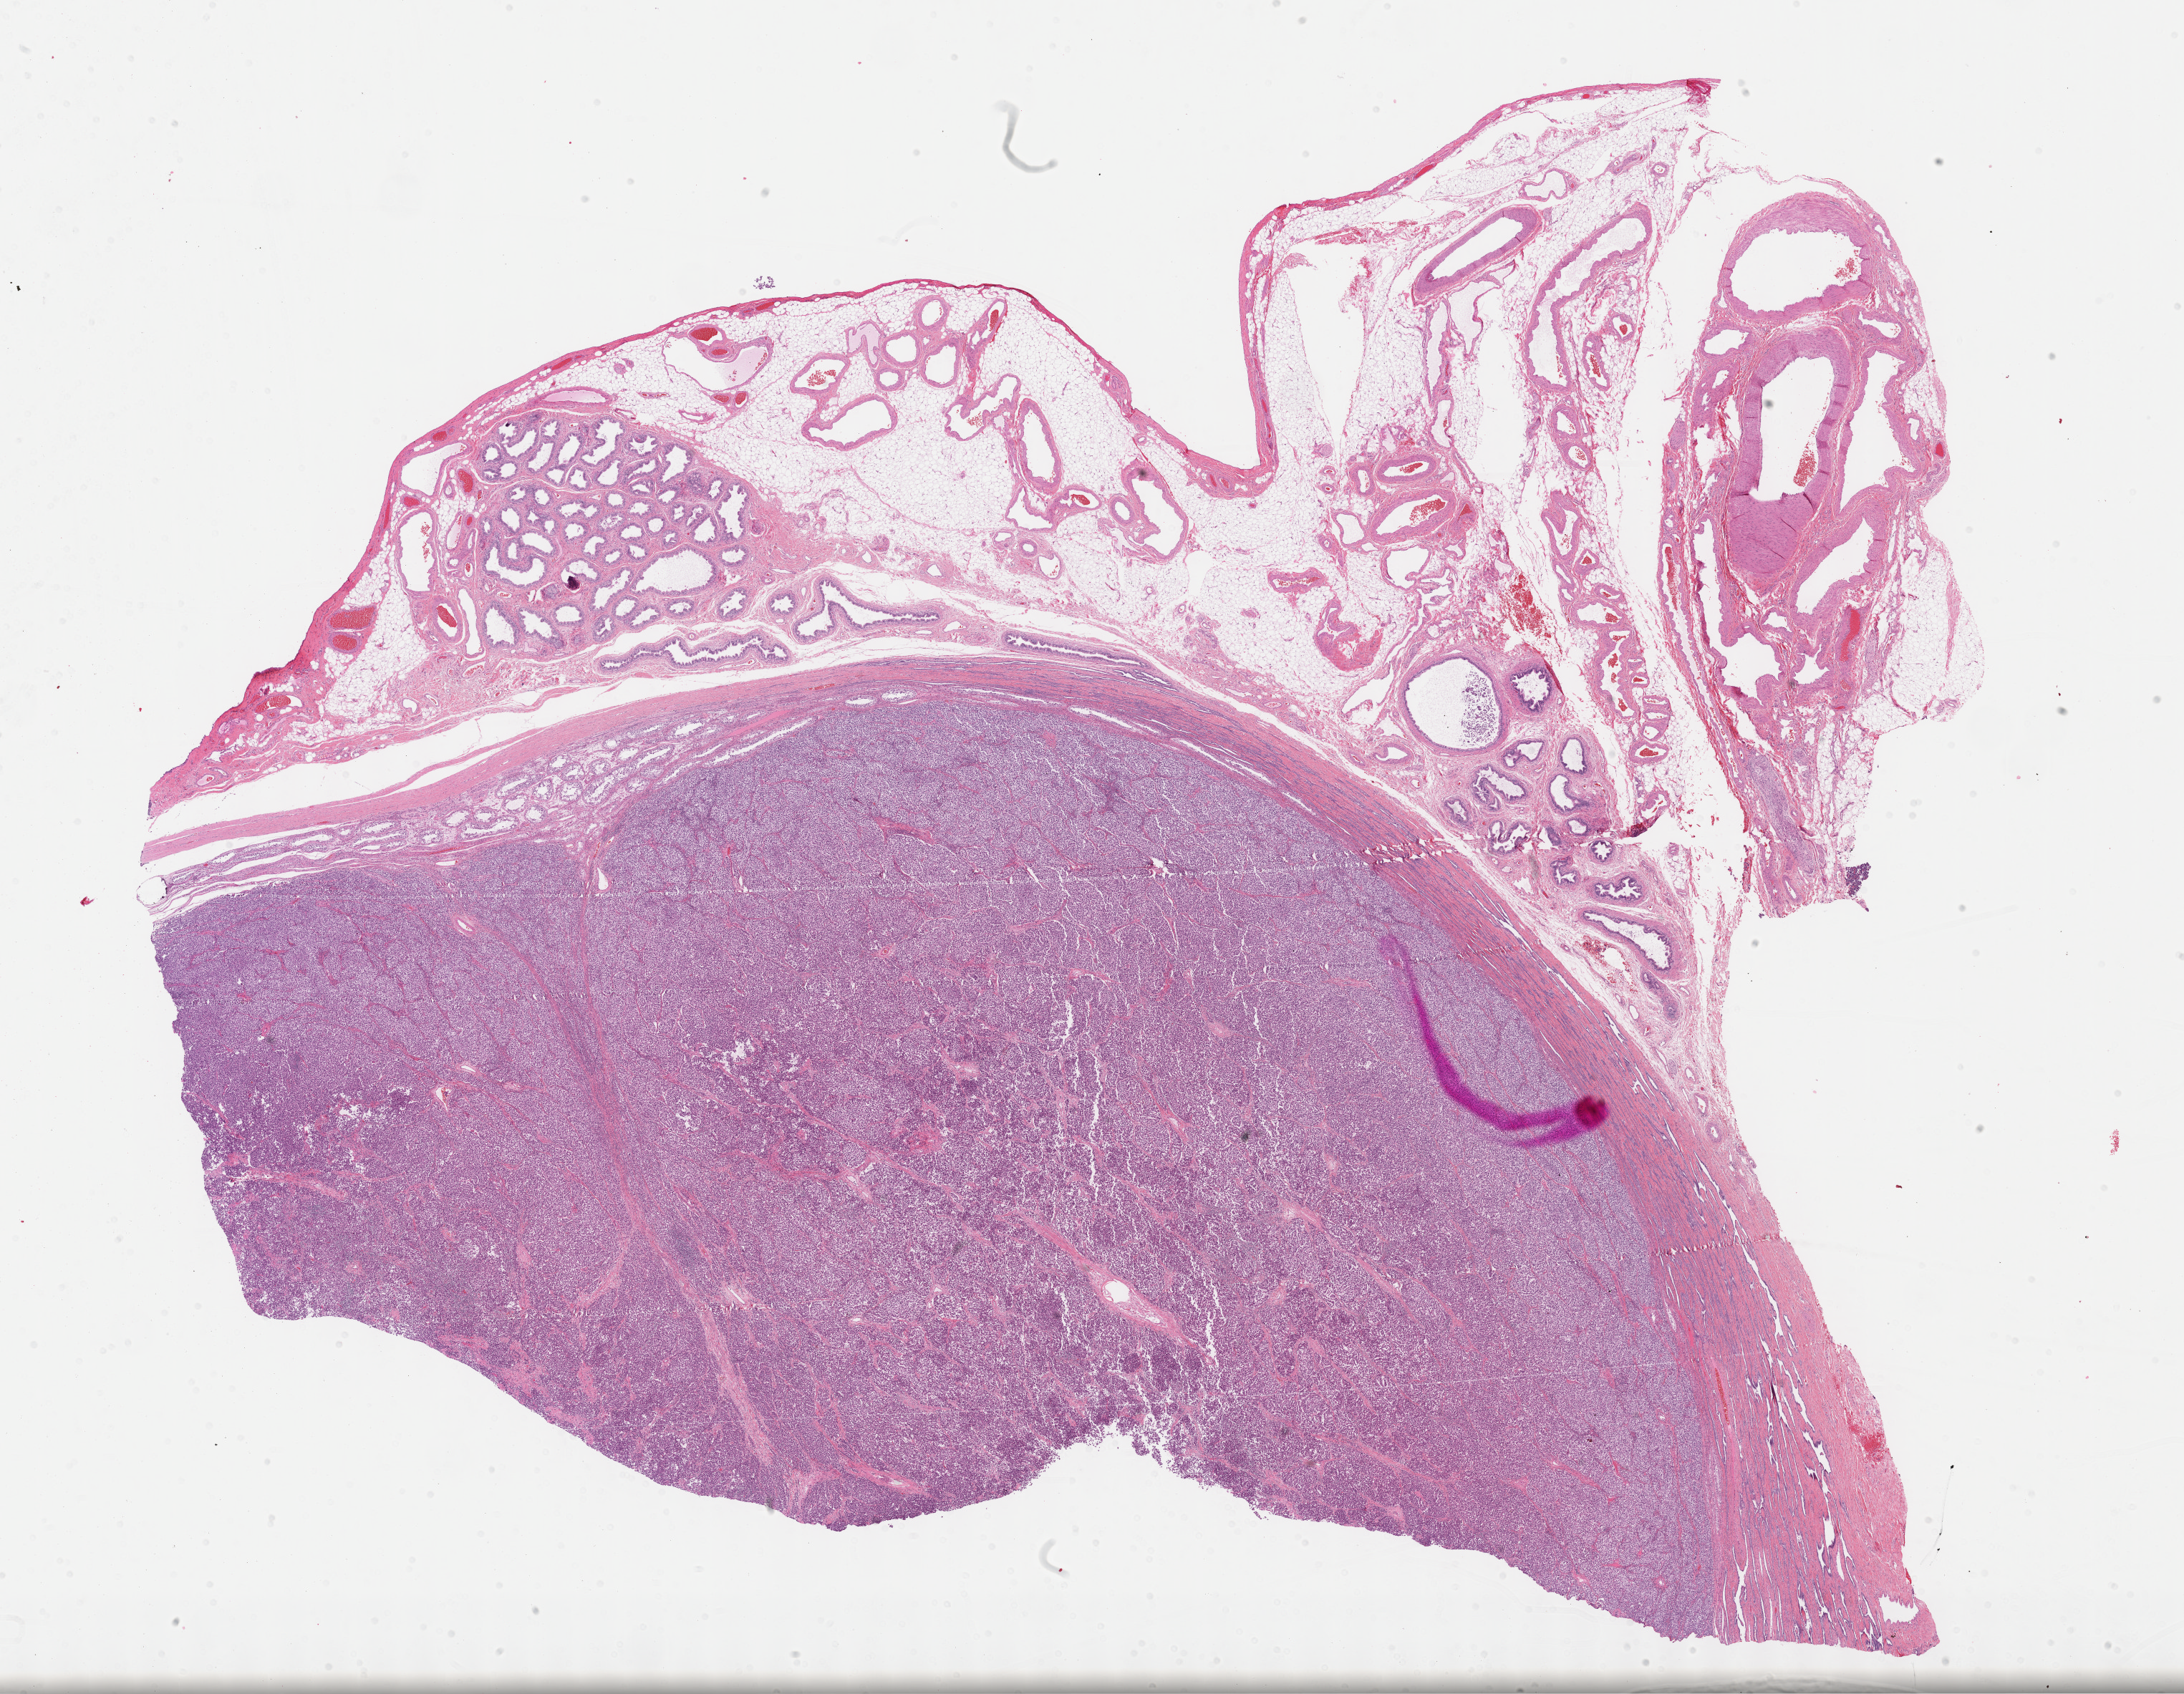
Whole-slide histology image, H&E-stained, a low-resolution overview of the entire scanned area, about 24.7 x 19.1 mm, FFPE section, testis, primary tumour sample. Patient: male, age at initial diagnosis 38 years.
Pathologic diagnosis: Seminoma, NOS.